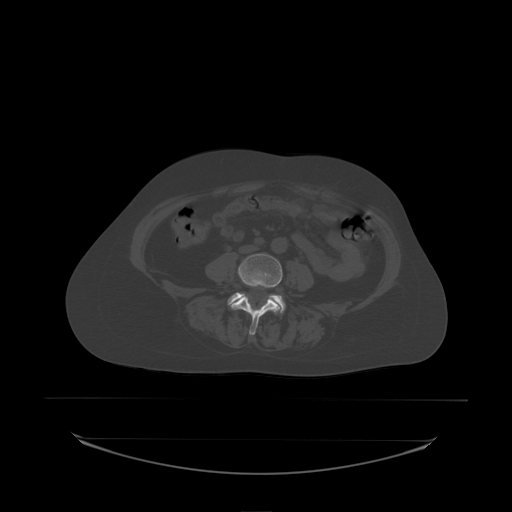
CT including the spine, one axial slice. Slice 47 of 242 in the series (ordered by position). Bone window (W 1800 / L 400 HU). 512 × 512 image matrix, field of view 500 × 500 mm. Patient: female, 53 years. Case-level facts recorded for this patient, not image findings: primary cancer: lung; vertebrae with lytic lesions (as recorded): T7, L1.
Outlined on this slice (semi-automatic segmentation, software-assisted and operator-edited):
- L4 vertebra: bounding box [x1, y1, x2, y2] px = [231, 254, 283, 335]
- L5 vertebra: [228, 293, 286, 314]